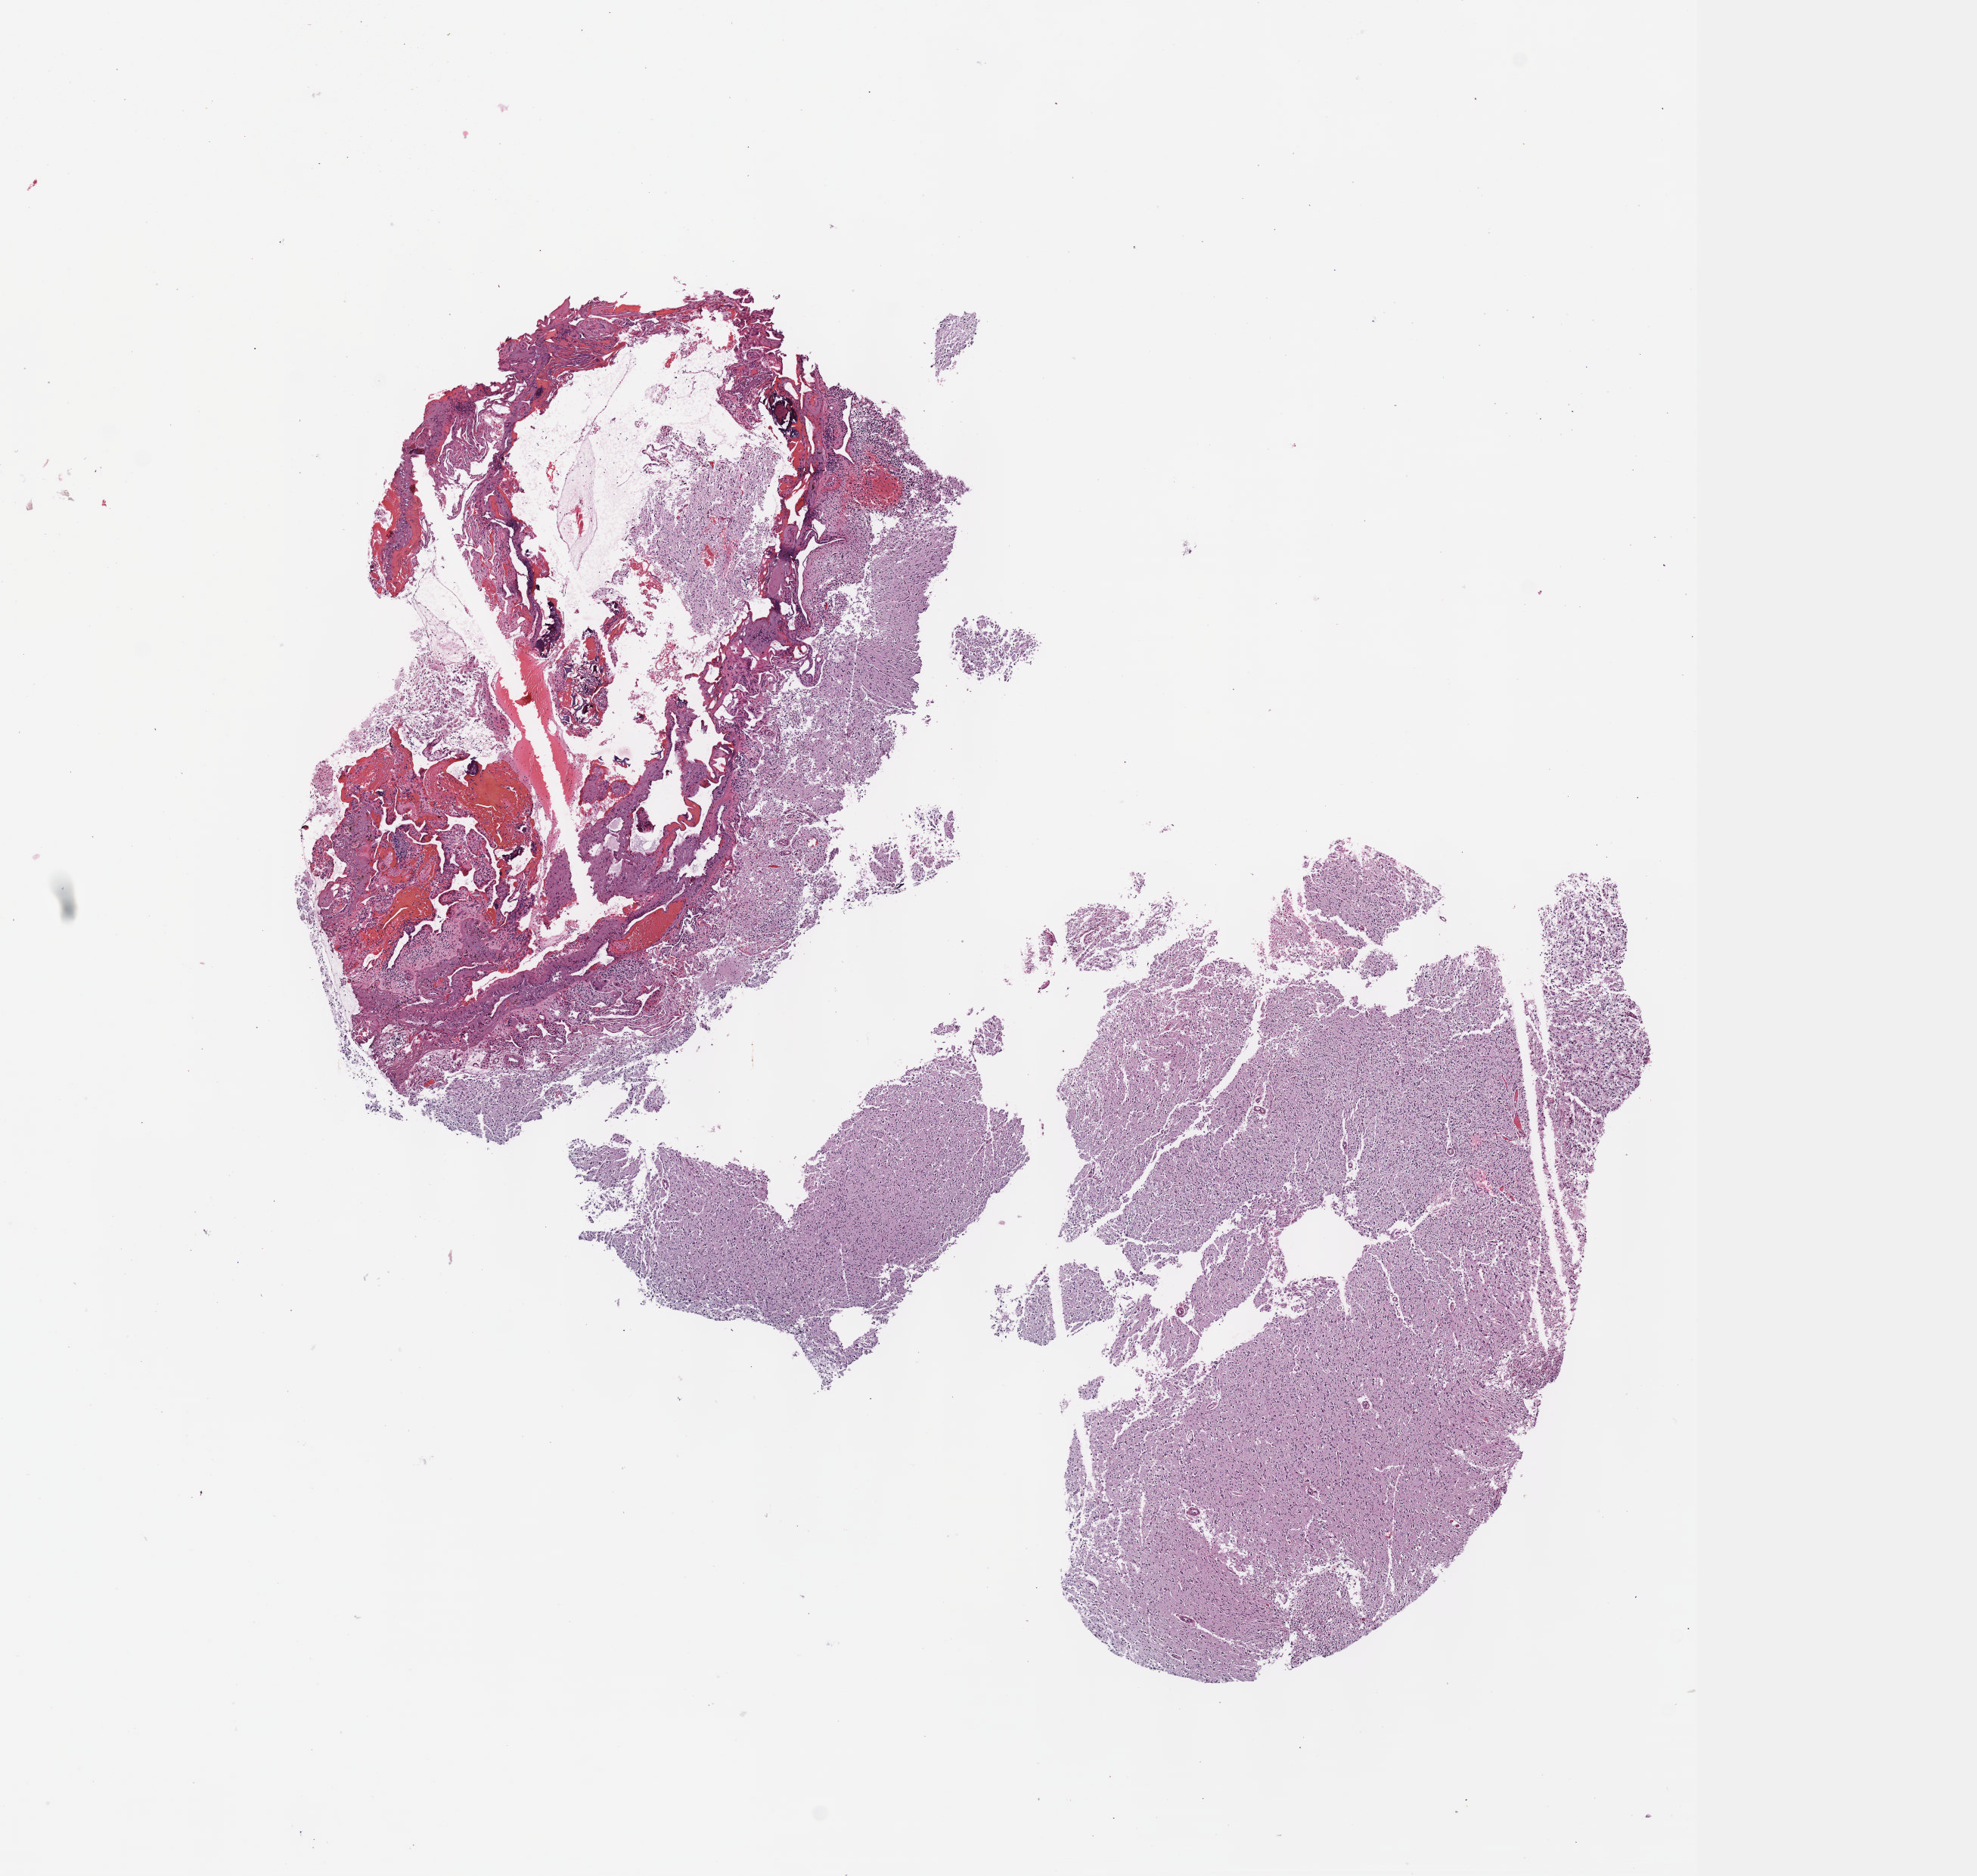
Whole-slide histology image, H&E-stained — shown as a low-resolution overview of the whole scanned area (about 10.6 x 10.0 mm, acquisition: 40x scan), FFPE section, sample: primary tumour, brain. Female, age 48 years at initial diagnosis. Histologic grade: G3 (poorly differentiated).
Diagnosis: Oligodendroglioma, anaplastic.